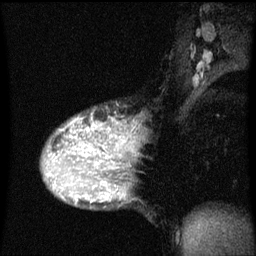
Breast MRI (dynamic contrast-enhanced), one sagittal slice; slice 37 of 60 in the series (ordered by position); dynamic contrast-enhanced series, image 2 of 3 at this slice position (ordered by acquisition); 1.5 T; TE 4.2 ms, TR 8 ms; 2 mm slice thickness; 256 × 256 image matrix. Patient: female, 36 years.
Outlined on this slice (semi-automatic segmentation, software-assisted and operator-edited):
- analysis volume of interest (the breast-tissue region the enhancement analysis was run in; not a lesion): bounding box [x1, y1, x2, y2] px = [42, 116, 124, 169]
- tumour enhancement mask (voxels above the 70 % enhancement threshold inside the analysis volume of interest): [58, 118, 121, 169]